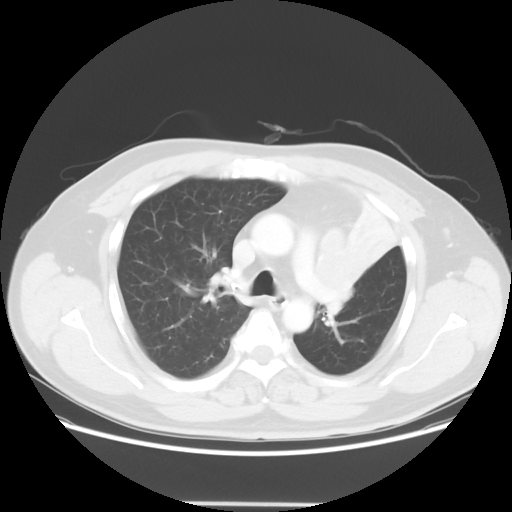
Chest CT, one axial slice; position 41 of 62 along the scan axis; reconstruction kernel STANDARD; lung window (W 1500 / L -600 HU); 512 × 512 image matrix. Patient: male, 49 years. Case-level facts recorded for this patient, not image findings: clinical TNM (as recorded): T3 N3 M1c.
Outlined on this slice (rectangle marked by the reading radiologist):
- lung tumour (recorded histology: squamous cell carcinoma): bounding box (x1, y1, x2, y2) in pixels: (310, 221, 363, 317)